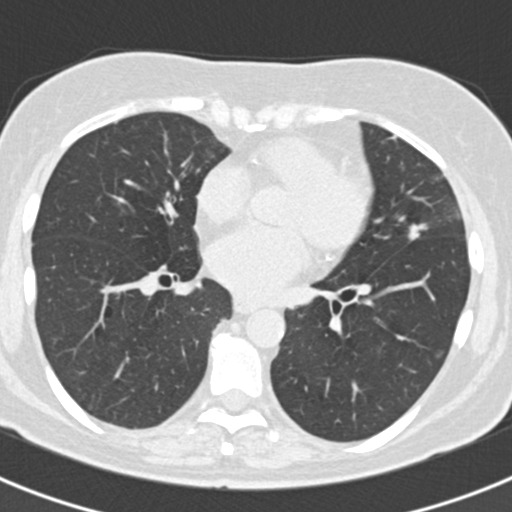
Low-dose screening chest CT, axial slice, baseline screening round, lung window (W 1500 / L -600 HU), 2 mm slice thickness, standard (soft-tissue) reconstruction kernel (B30f), 512 × 512 image matrix. Female, age 60 years at enrolment. Current smoker at enrolment.
Expert reader's lesion annotation, bounding box <398,215,435,249> (left, top, right, bottom; pixels). The screening reader recorded 3 non-calcified nodules or masses ≥4 mm on this exam (lingula, left lower lobe, lingula); which of them this box marks is not recorded. Official screen result: positive, change unspecified: nodule(s) >= 4 mm or enlarging nodule(s), mass(es), or other non-specific abnormalities suspicious for lung cancer. Participant outcome: lung cancer diagnosed 886 days after this screen — non-small cell carcinoma, left upper lobe, poorly differentiated (G3), stage IB (AJCC 6th edition), 7 mm at pathology.